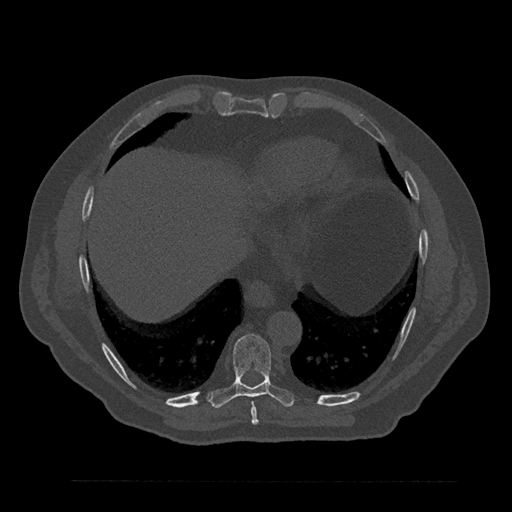
CT including the spine, one axial slice; reconstruction kernel Br40s/3; 120 kVp; bone window (W 1800 / L 400 HU); 0.5 mm slice thickness; 512 × 512 image matrix, field of view 430 × 430 mm. Male patient, age 61 years. From the clinical record (not read from this slice): primary cancer: prostate.
Outlined on this slice (semi-automatically segmented with operator editing):
- T8 vertebra: bounding box <251,402,259,425> (left, top, right, bottom; pixels)
- T9 vertebra: <208,334,295,408>